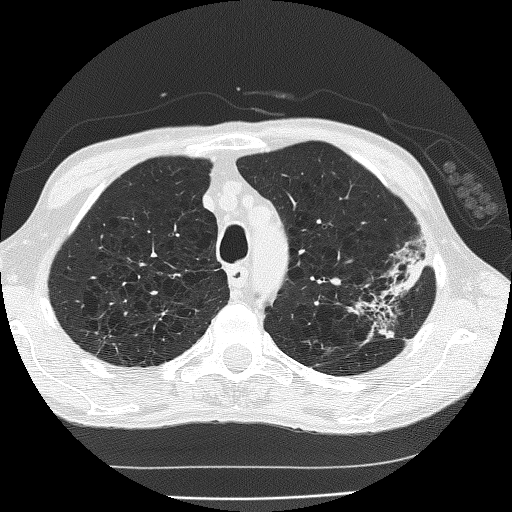
Chest CT (low-dose screening protocol), one axial image; second annual screen; lung window (W 1500 / L -600 HU); 2 mm slice thickness; lung (sharp) reconstruction kernel (FC51); 120 kVp; 512 × 512 image matrix. Male participant, aged 60 years at enrolment. Current smoker at enrolment.
Expert reader's lesion annotation, bounding box (x1, y1, x2, y2) in pixels: (346, 251, 434, 338). The screening reader recorded 2 non-calcified nodules or masses ≥4 mm on this exam; which of them this box marks is not recorded. Official screen result: positive, other. Later outcome: lung cancer diagnosed 178 days after this screen — bronchiolo-alveolar carcinoma, mucinous, left upper lobe, stage IV (AJCC 6th edition).